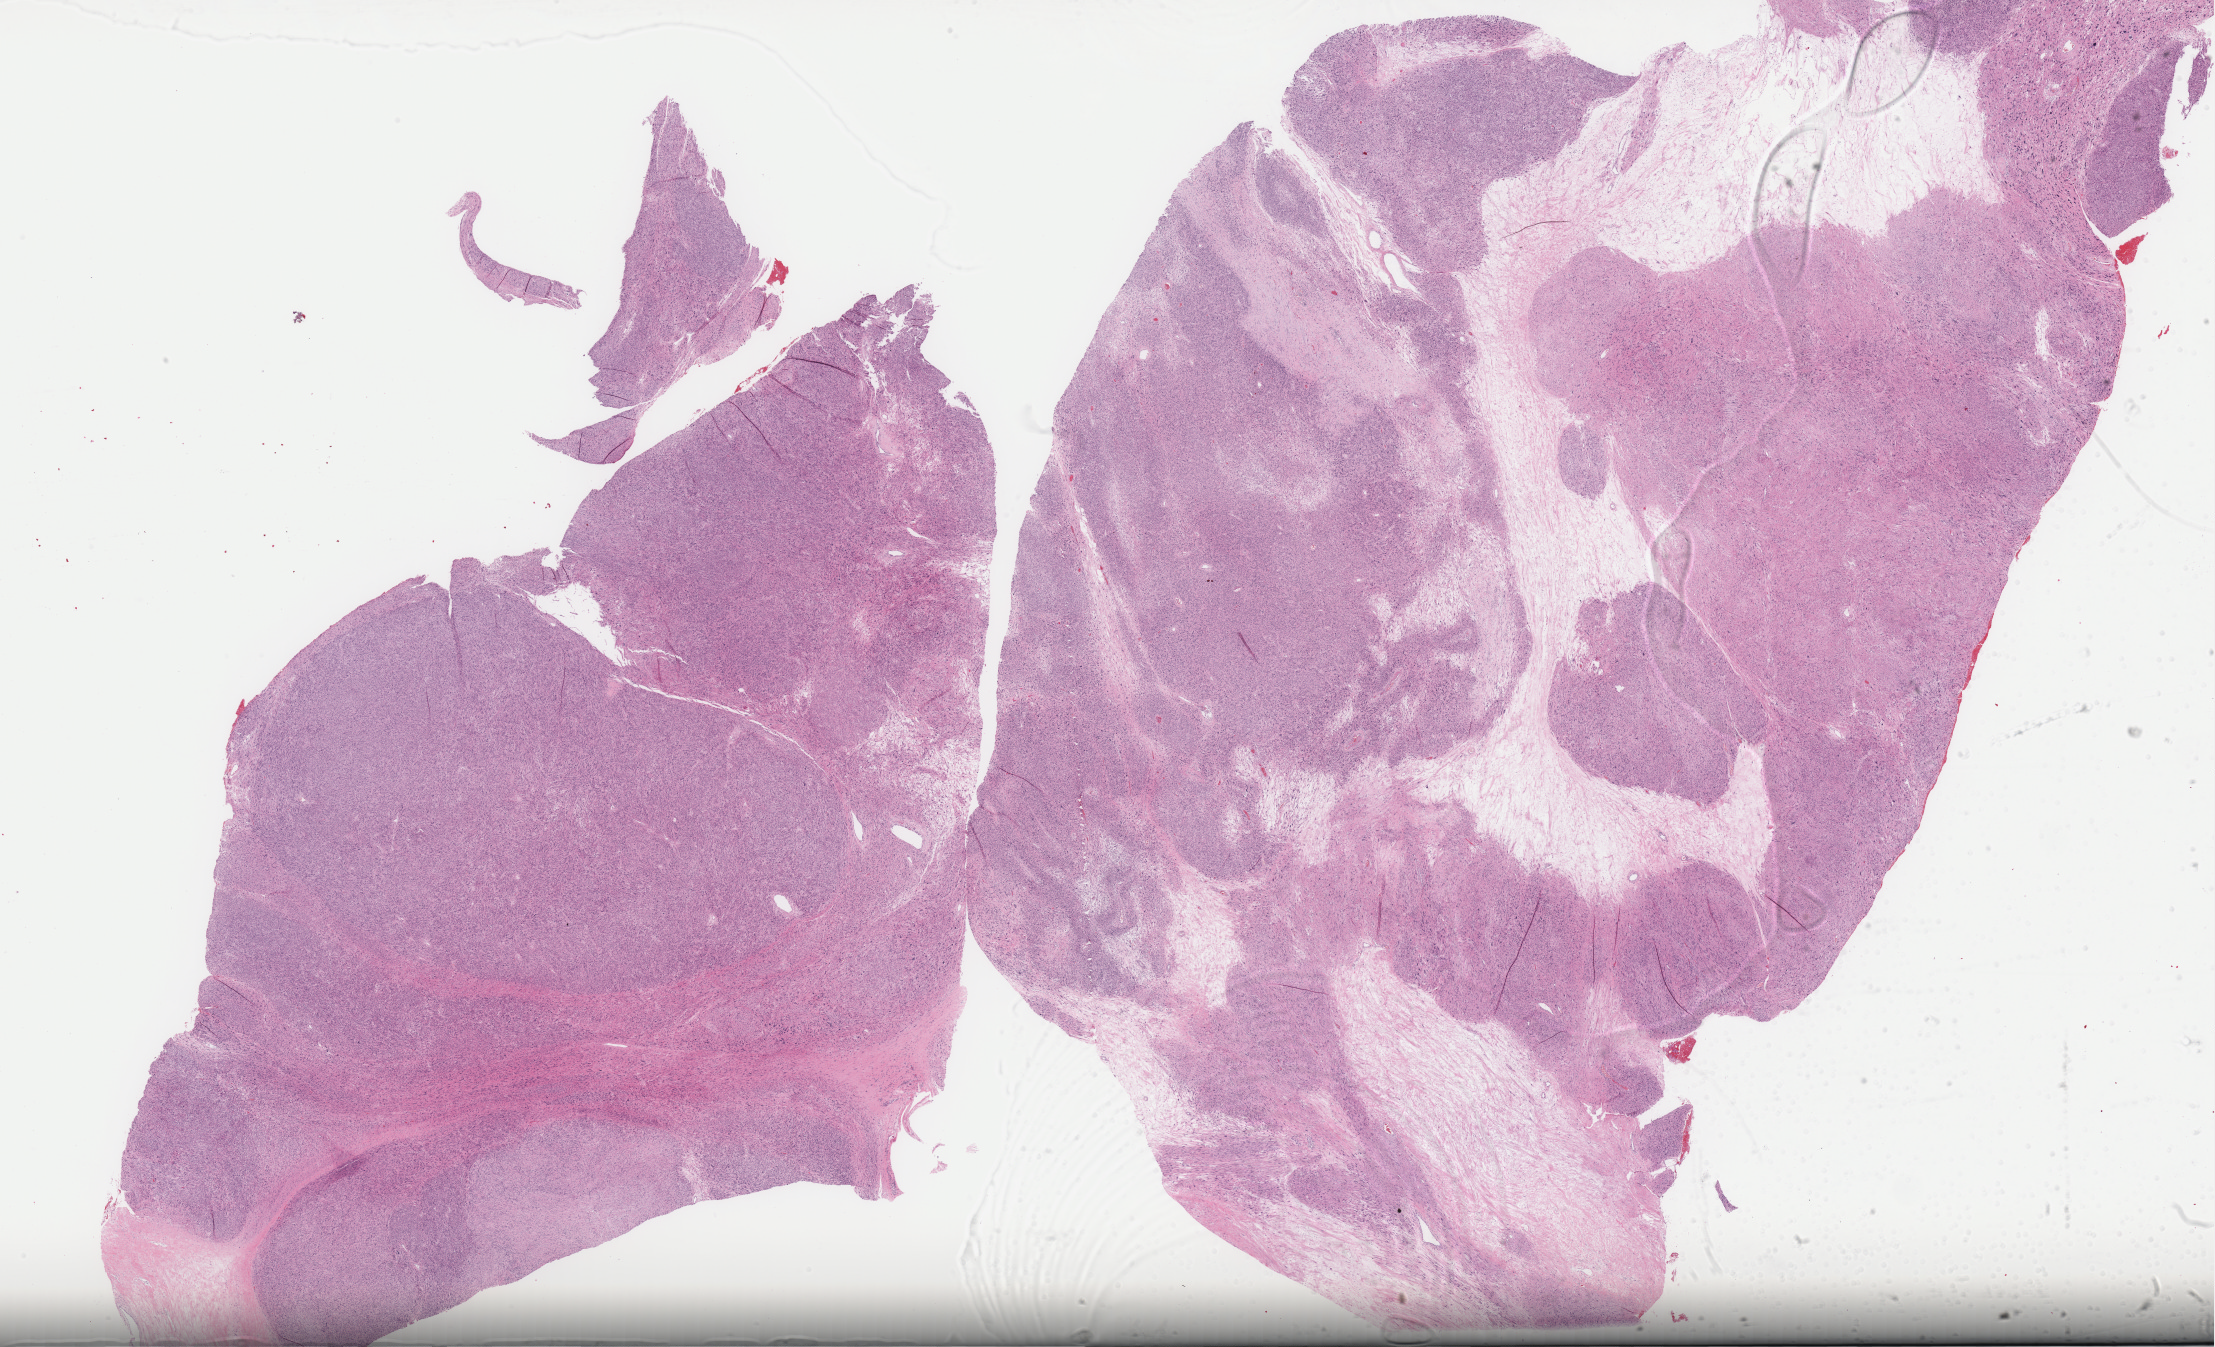
Digitized H&E tissue section (whole slide) — whole scanned area (about 35.4 x 21.5 mm) shown as a low-resolution overview. Formalin-fixed paraffin-embedded (FFPE) diagnostic section. Retroperitoneum and peritoneum, primary tumour sample. Male patient; age at initial diagnosis 55 years.
Histologic diagnosis: Leiomyosarcoma, NOS (retroperitoneum).